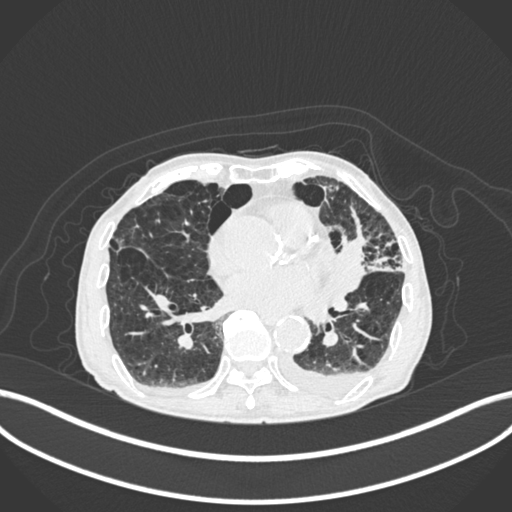
Chest CT, one axial slice. Slice 85 of 400 in the series (ordered by position). Lung window (W 1500 / L -600 HU). 512 × 512 image matrix. Male patient, age 90 years or older. Case-level facts recorded for this patient, not image findings: clinical TNM (as recorded): T2b N1 M0.
Annotated regions visible in this slice (bounding box drawn by a radiologist):
- lung tumour (recorded histology: squamous cell carcinoma): bounding box <332,221,365,296> (left, top, right, bottom; pixels)